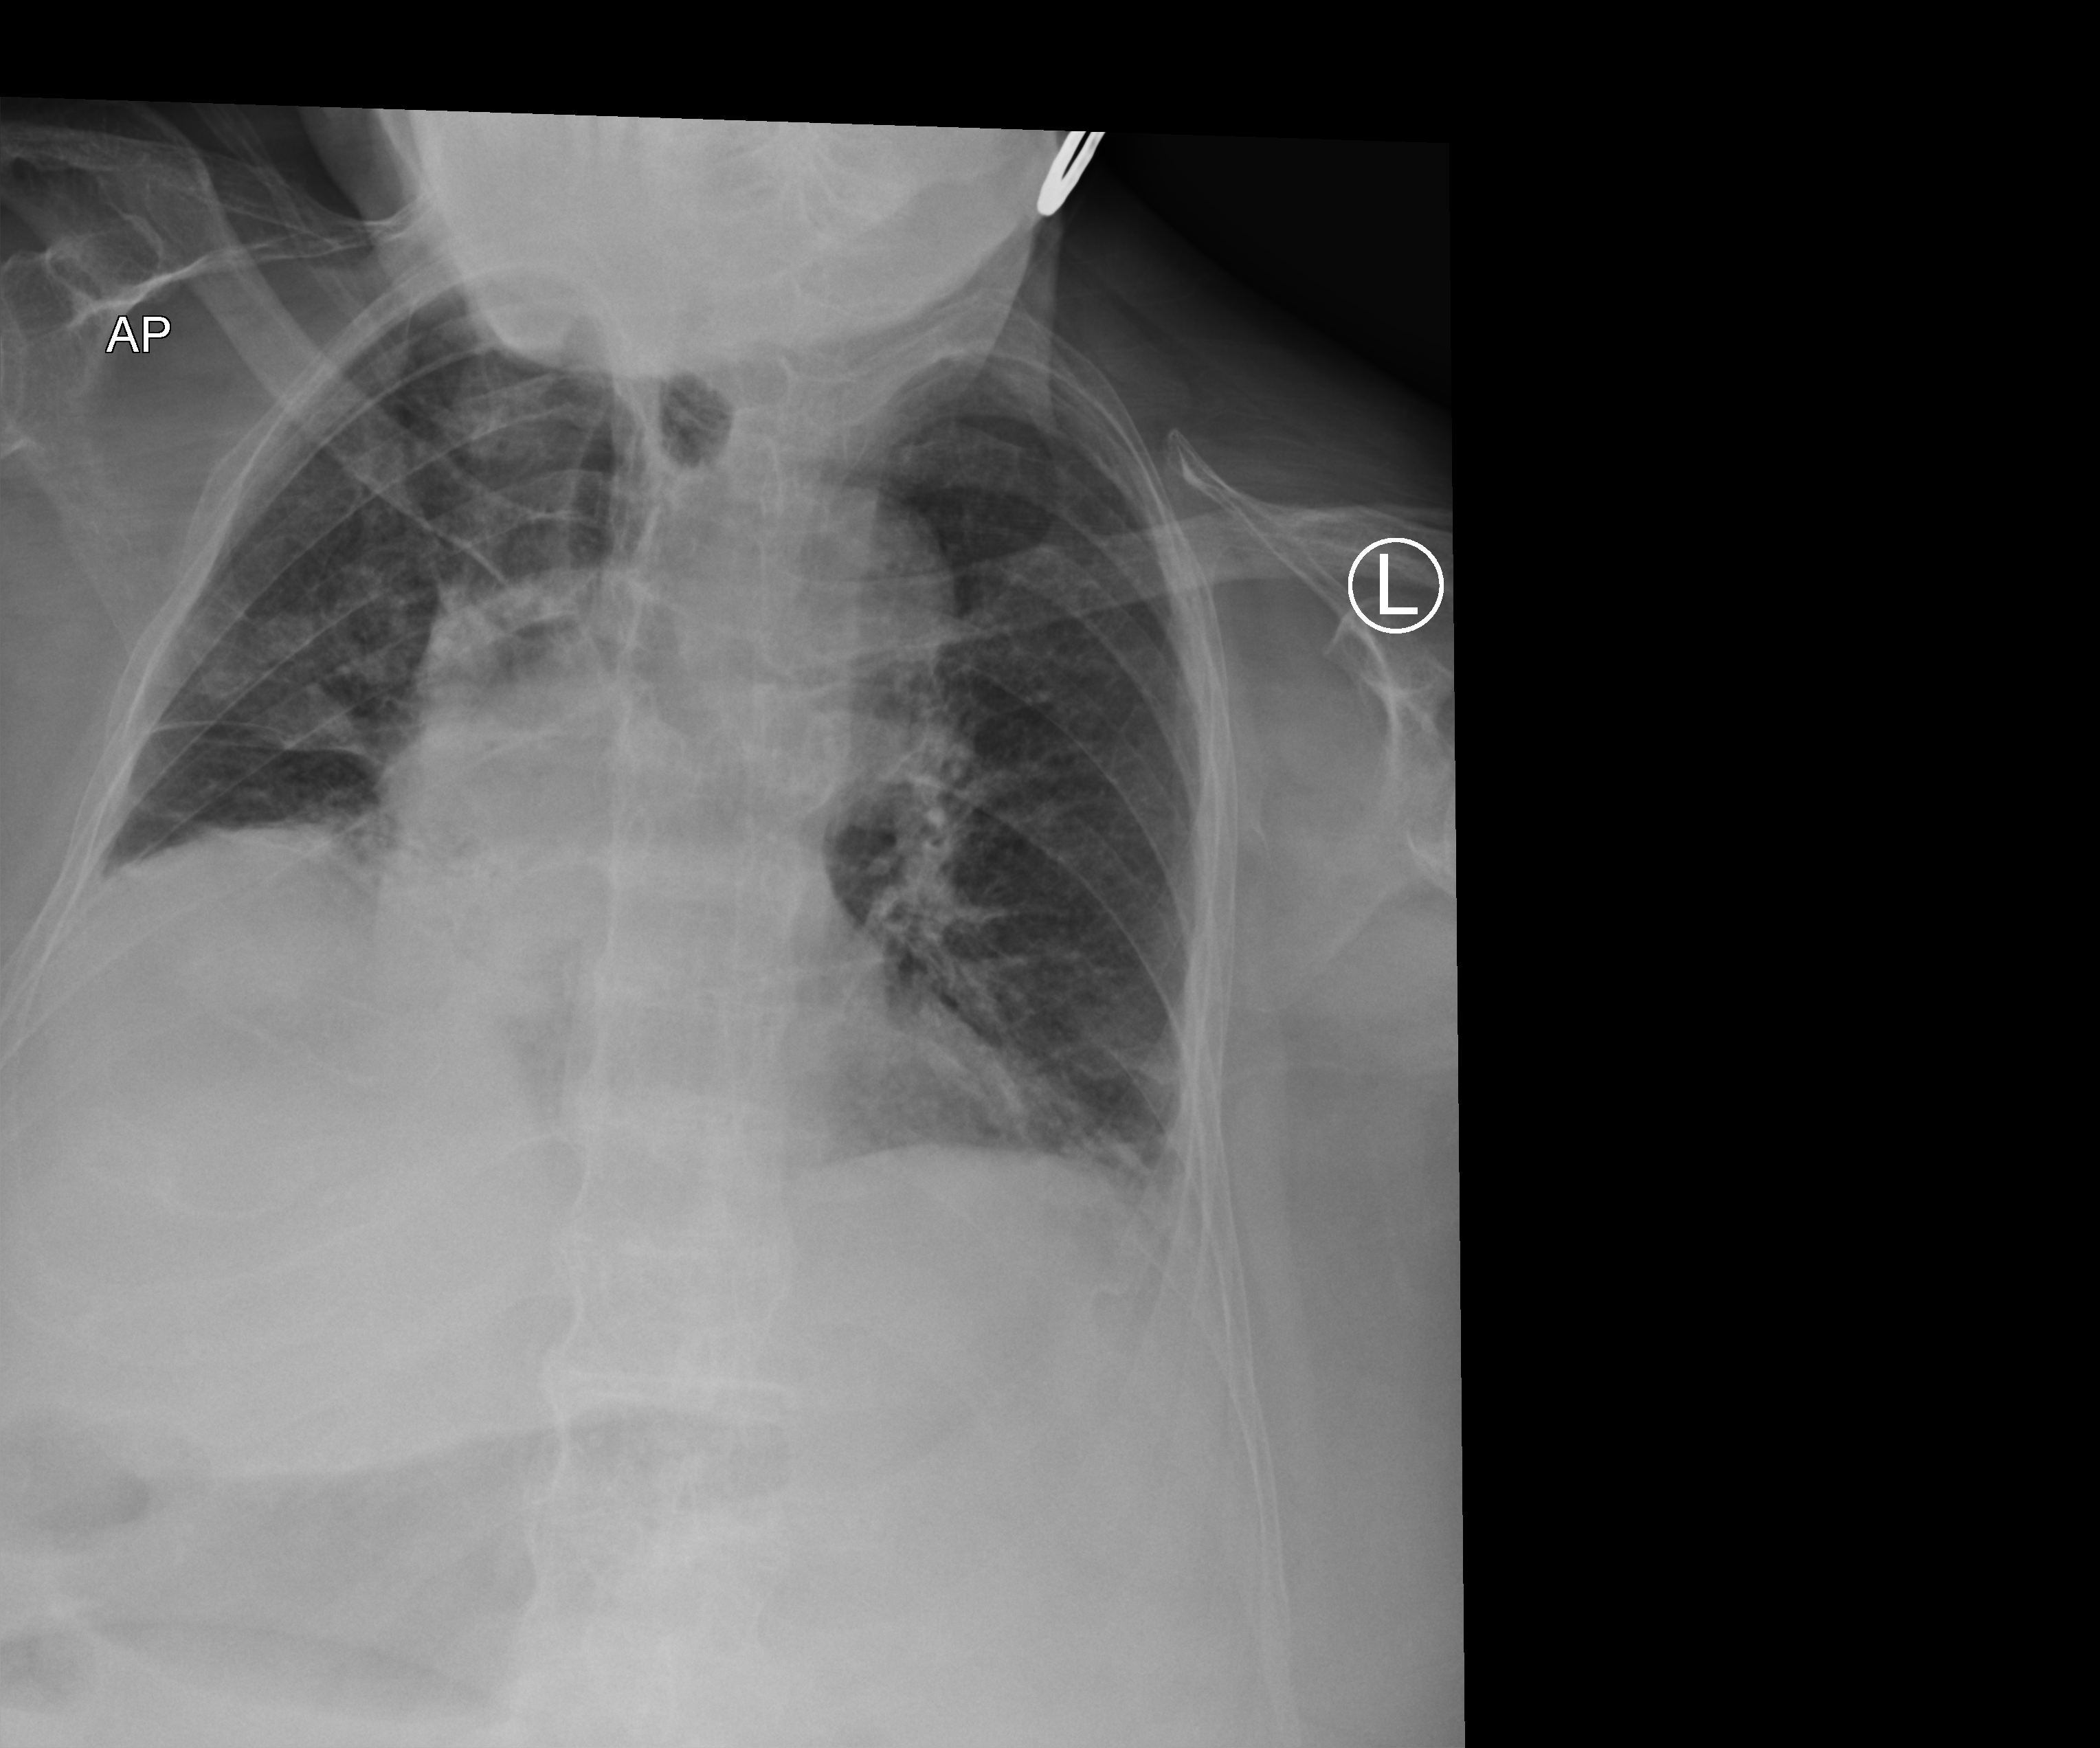
Portable chest radiograph; anteroposterior (AP) projection. Patient hospitalised with COVID-19; female, aged 75–90 years.
Admission-level facts for this patient (not findings on this image; timing relative to this image not recorded):
- hypertension (admission record): yes